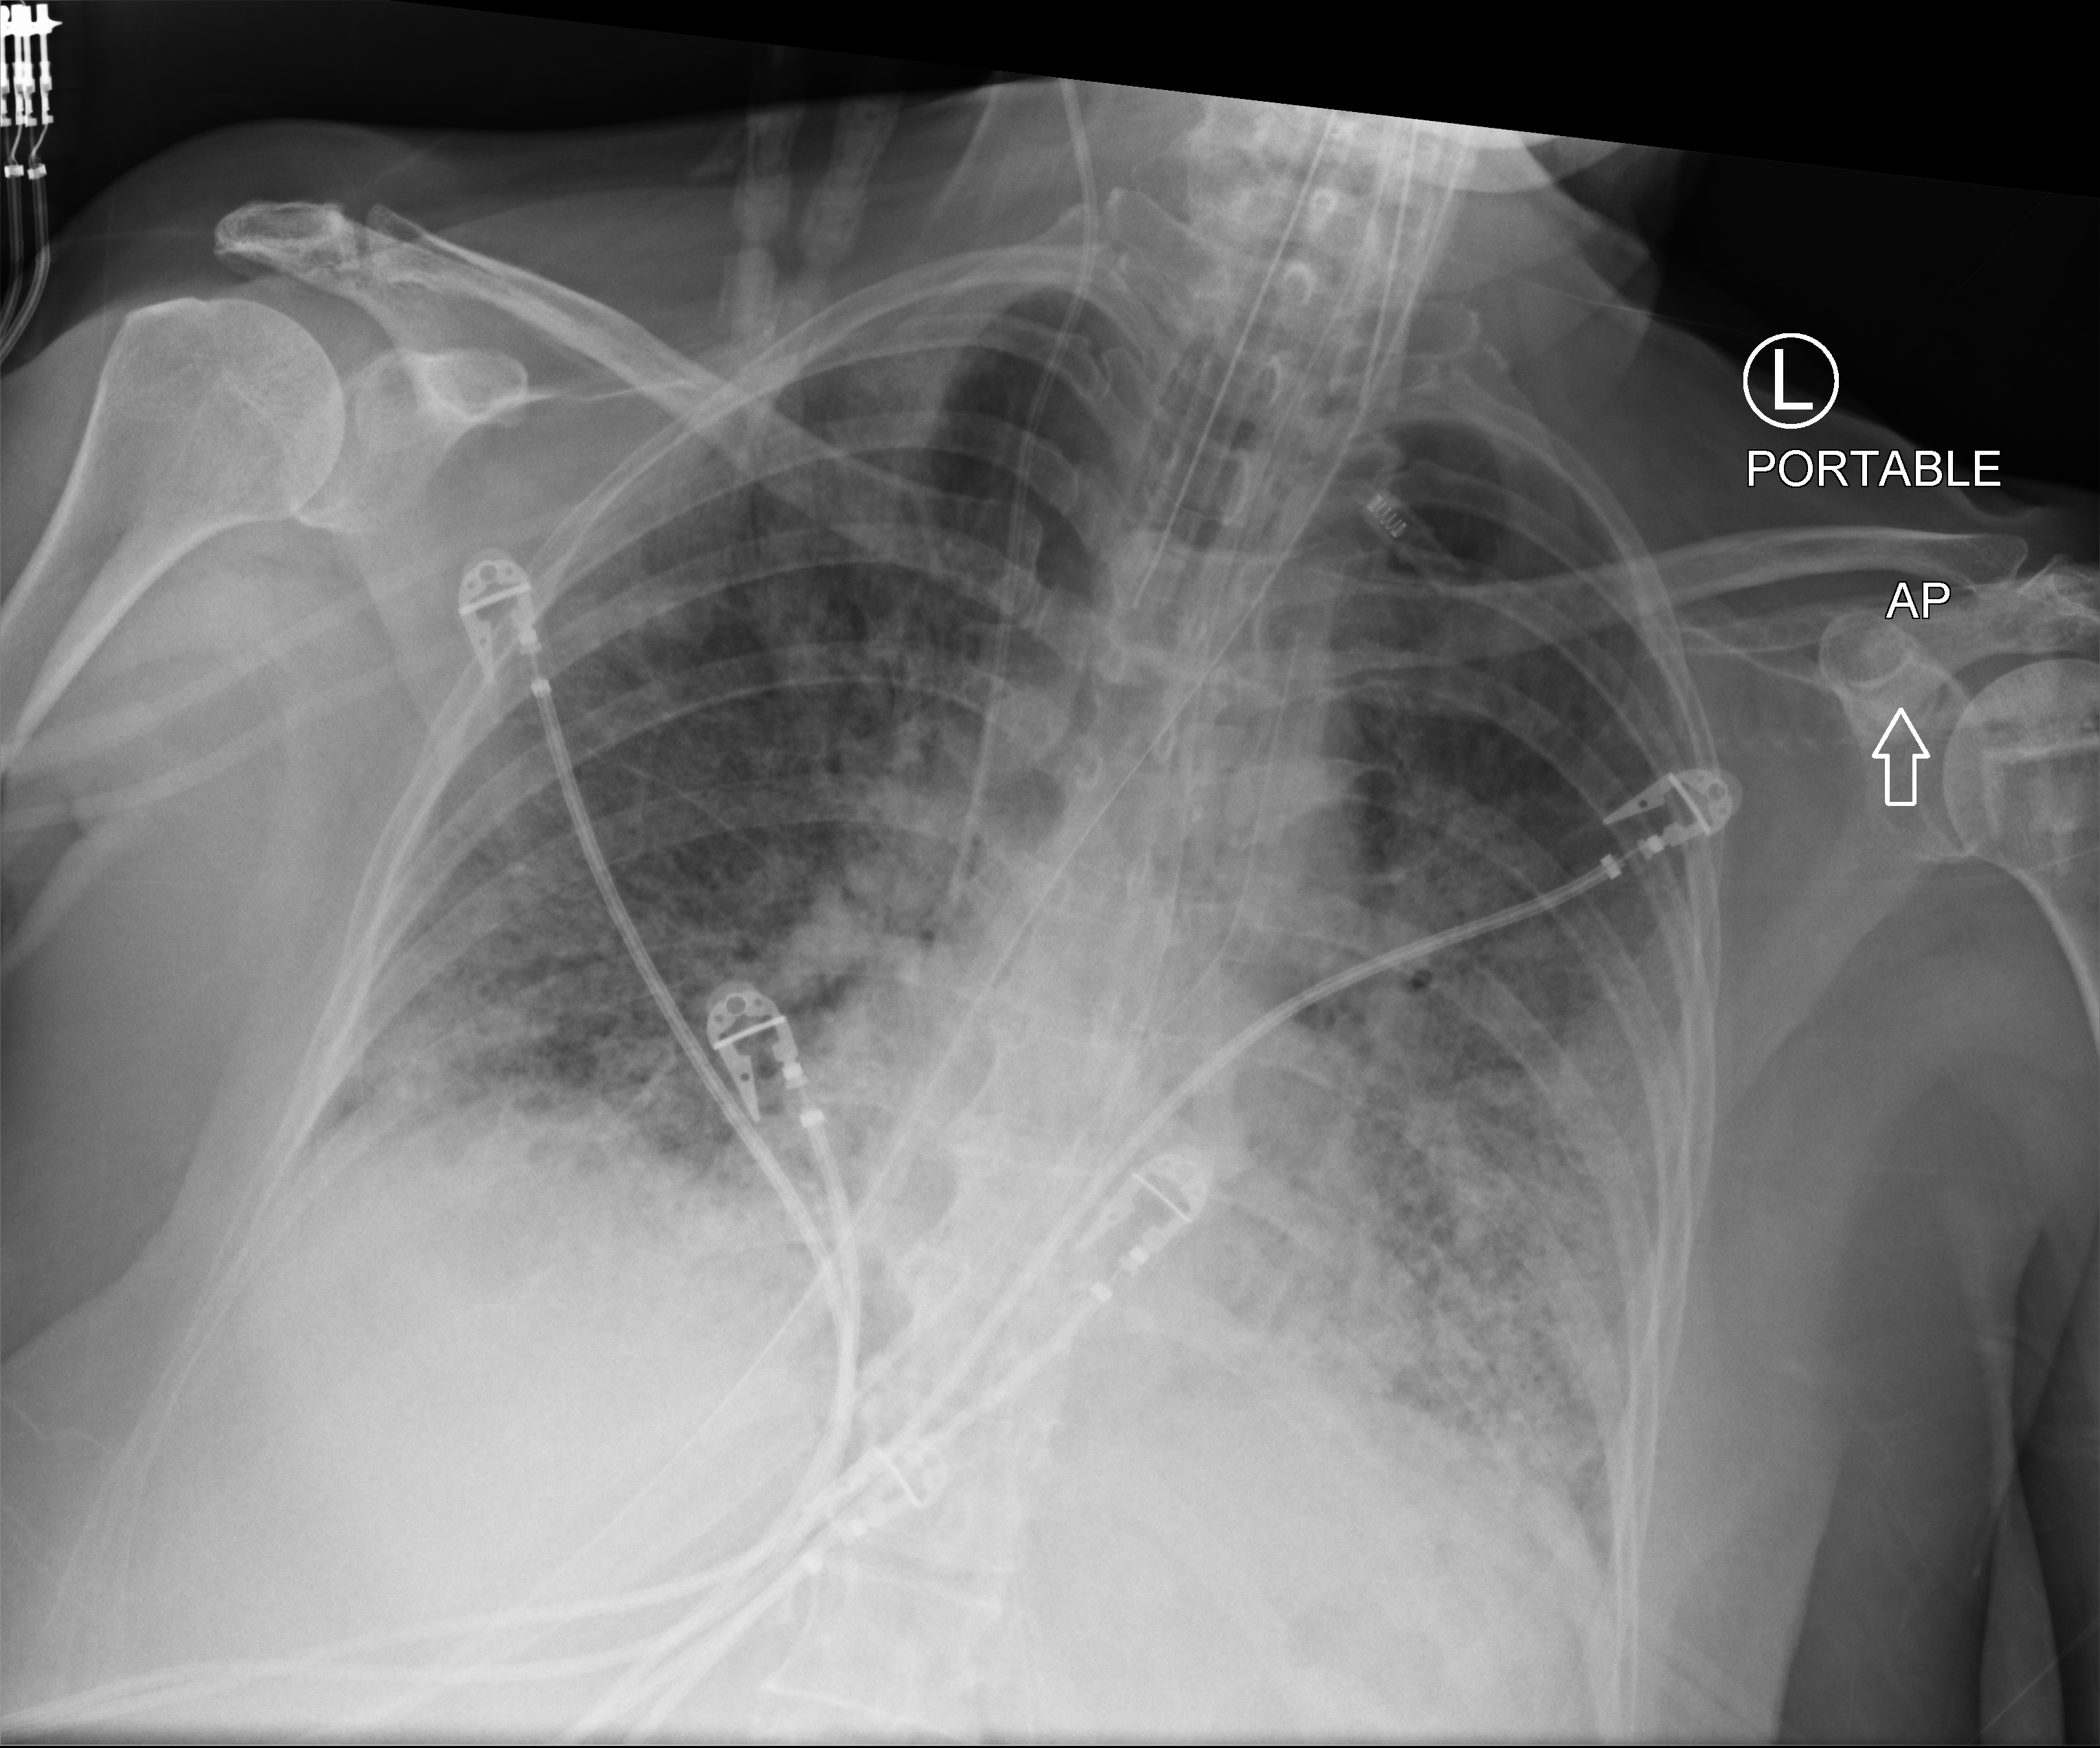
Chest X-ray (portable), anteroposterior (AP) projection. Patient hospitalised with COVID-19; female, aged 60–74 years.
Hospital-stay facts (about this admission, not read from this image; timing relative to this image not recorded):
- admitted to intensive care during this hospital stay: yes